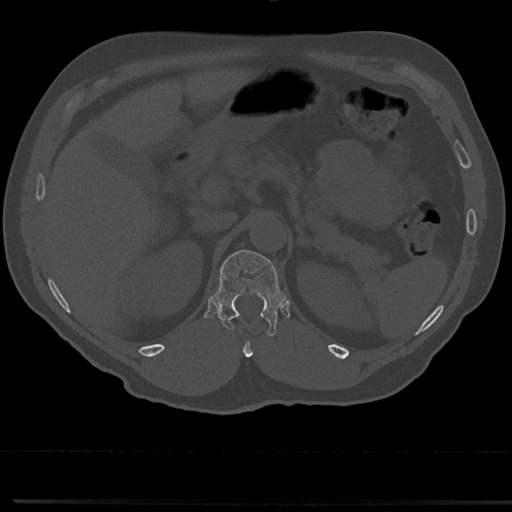
CT including the spine, one axial slice. Slice 157 of 817 in the series (ordered by position). 120 kVp. Bone window (W 1800 / L 400 HU). 0.5 mm slice thickness. 512 × 512 image matrix. Patient: male, 61 years. Case-level facts recorded for this patient, not image findings: primary cancer: prostate.
Structures marked on this image (semi-automatic segmentation, software-assisted and operator-edited):
- T12 vertebra: box from (x=216, y=248) to (x=282, y=334) px